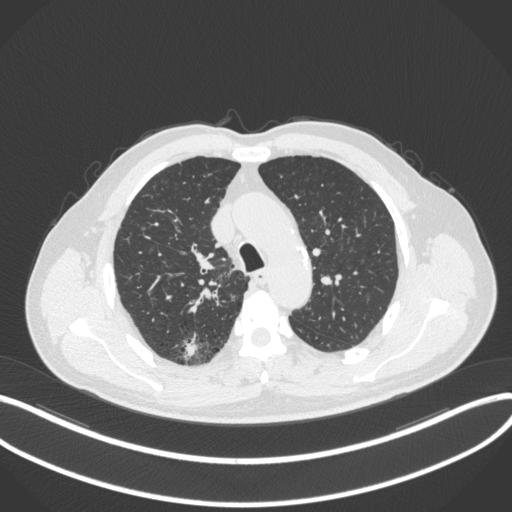
Chest CT, one axial slice. Position 272 of 366 along the scan axis. Reconstruction kernel B31f. Lung window (W 1500 / L -600 HU). 512 × 512 image matrix, field of view 400 × 400 mm. Male patient, age 69 years. Case-level facts recorded for this patient, not image findings: clinical TNM (as recorded): T1b N0 M0.
Outlined on this slice (rectangle marked by the reading radiologist):
- lung tumour (recorded histology: adenocarcinoma): bounding box [x1, y1, x2, y2] px = [180, 331, 197, 362]